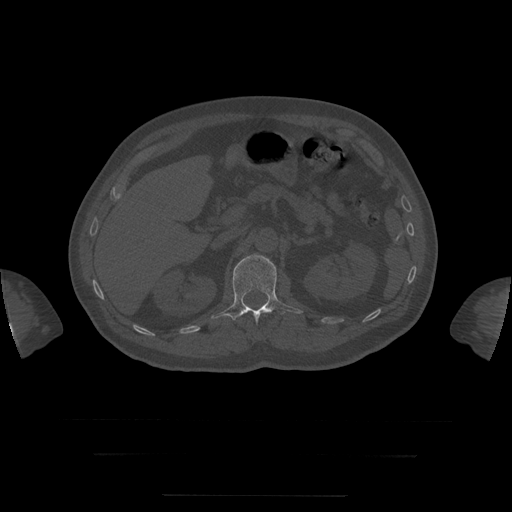
CT including the spine, one axial slice. Reconstruction kernel STANDARD. 120 kVp. Bone window (W 1800 / L 400 HU). 1.25 mm slice thickness. 512 × 512 image matrix. Patient age 73 years. From the clinical record (not read from this slice): primary cancer: prostate.
Annotated regions visible in this slice (semi-automatic segmentation, software-assisted and operator-edited):
- L1 vertebra: box from (x=212, y=255) to (x=303, y=322) px
- T8 vertebra: (x=235, y=307)–(x=269, y=320)